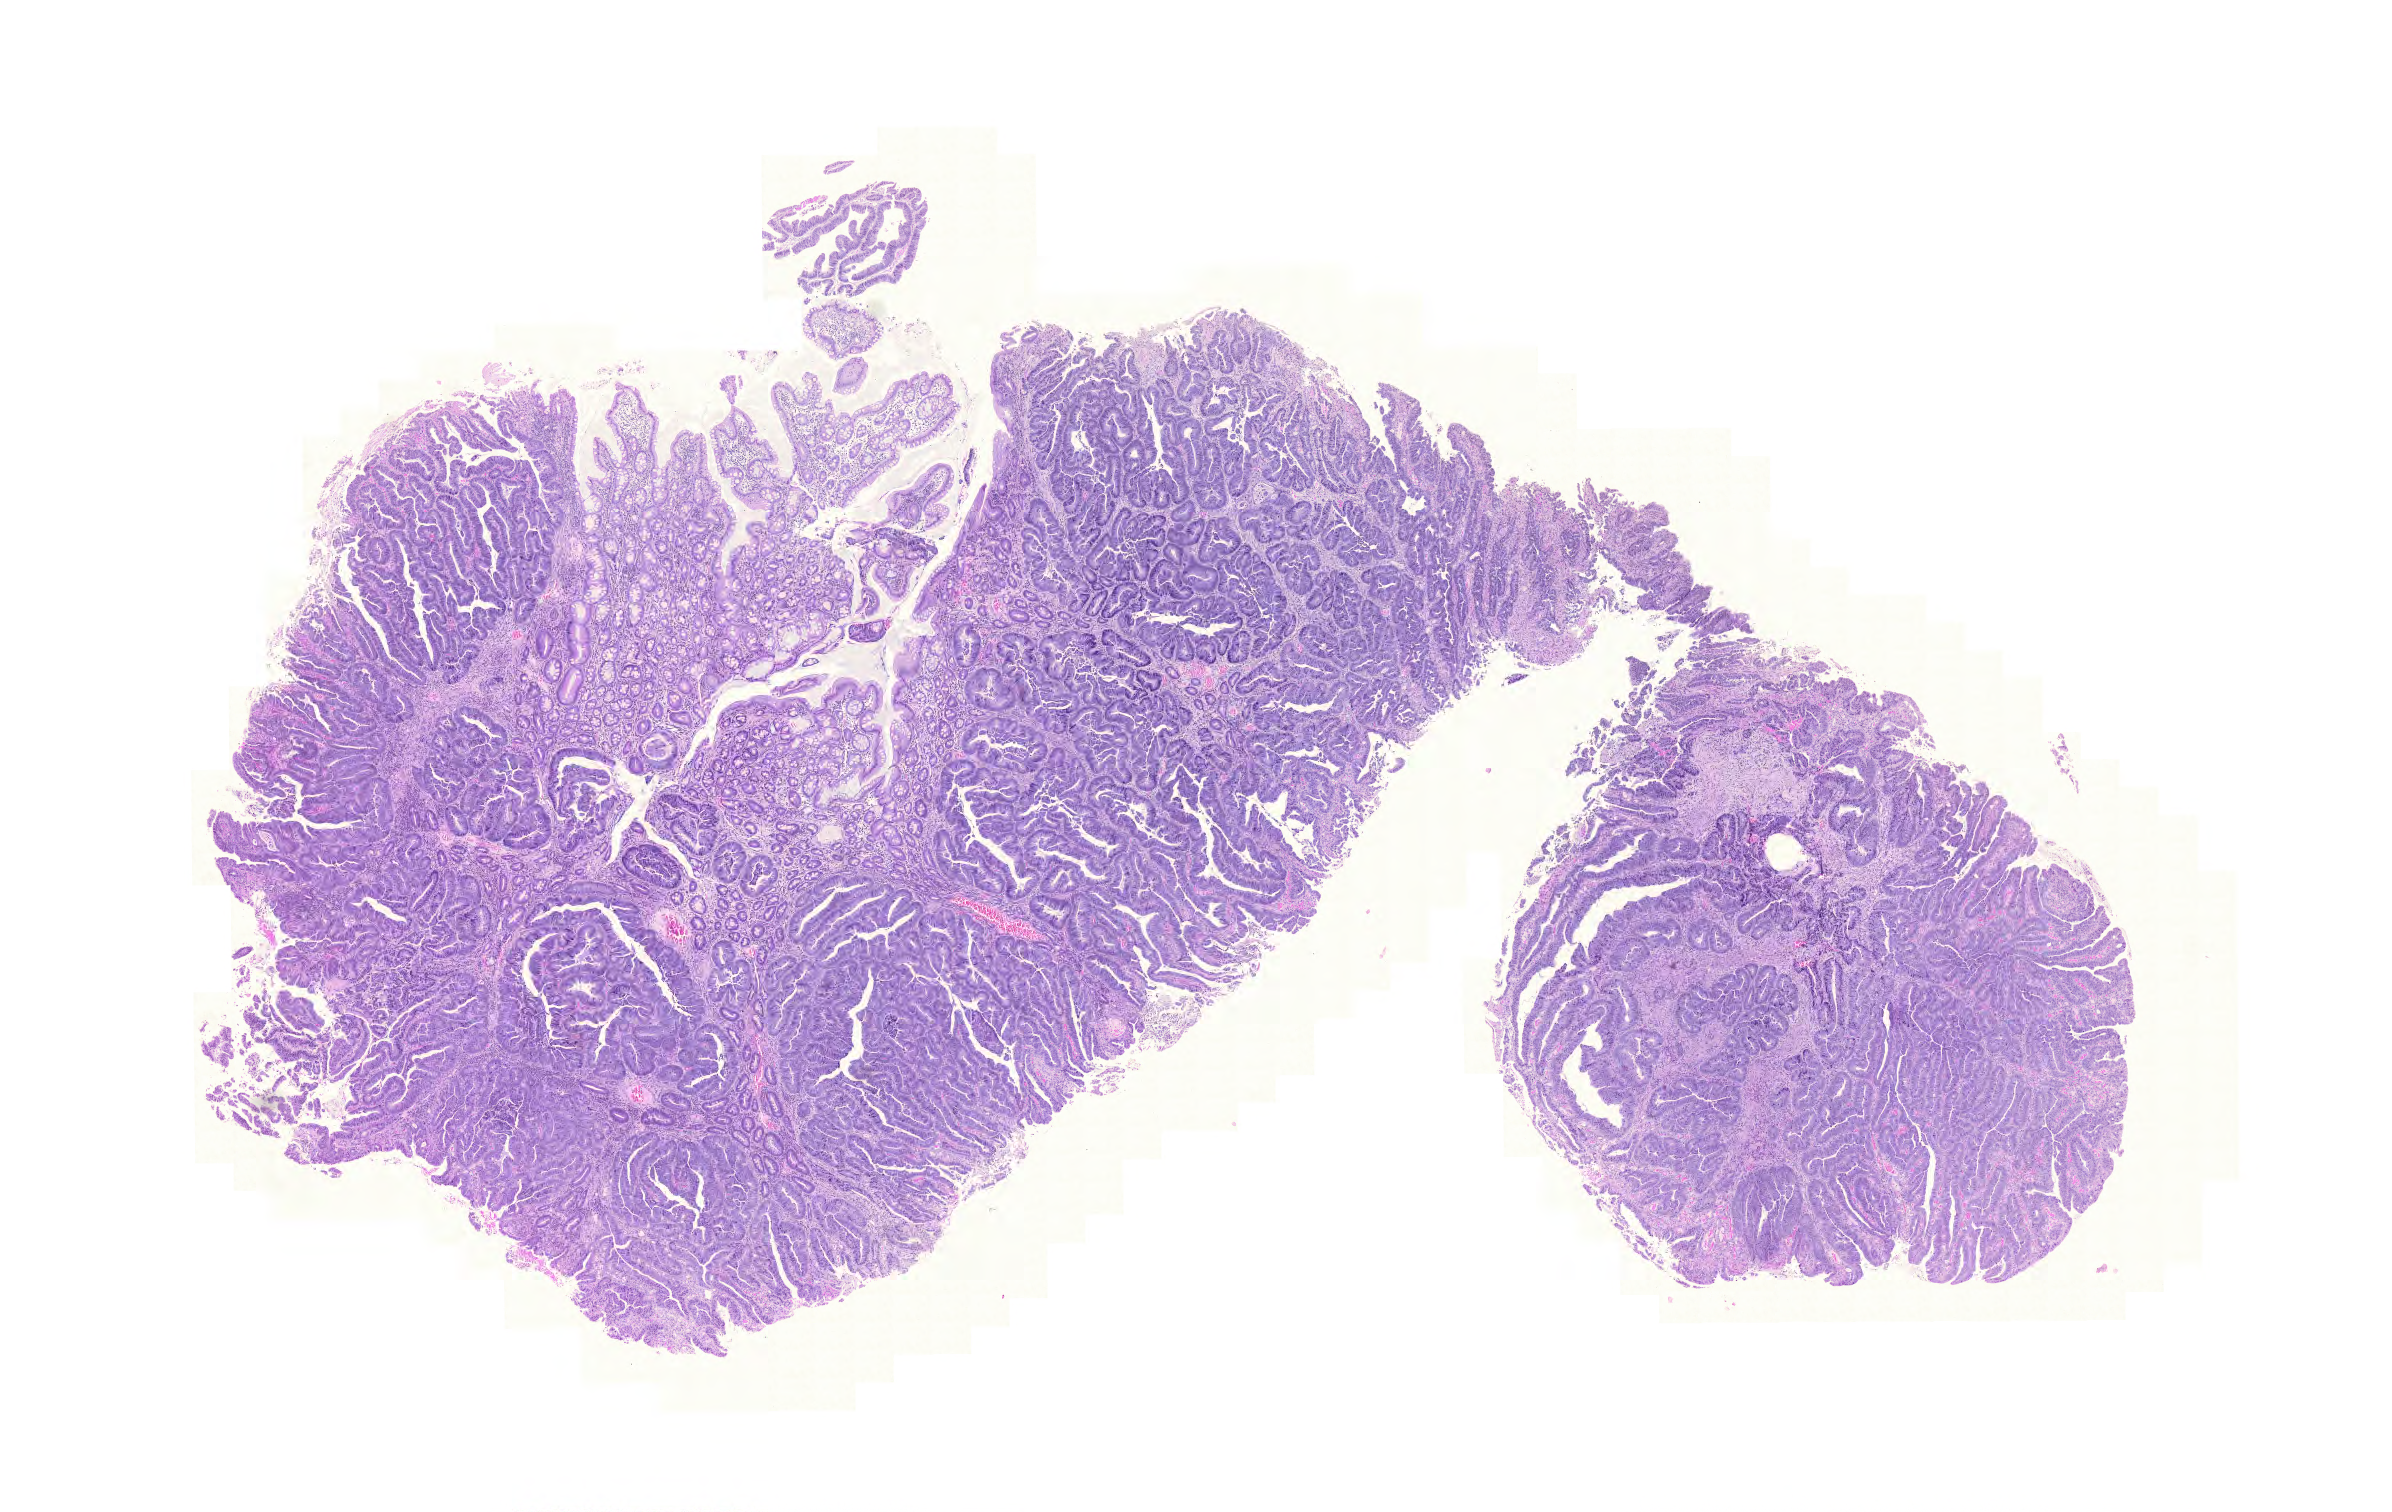
H&E whole-slide image, a low-resolution overview of the entire scanned area, about 17.8 x 11.2 mm, formalin-fixed paraffin-embedded (FFPE) diagnostic section, sample: primary tumour, colon. Patient: female, age at initial diagnosis 63 years.
AJCC pathologic stage: IV (6th edition). Histologic diagnosis: Adenocarcinoma, NOS (cecum). TNM: T3 N2 M1.